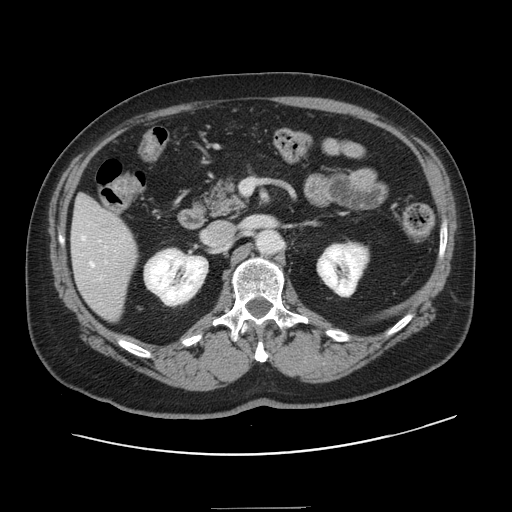
Contrast-enhanced abdominal CT, one axial slice; position 64 of 143 along the scan axis; 120 kVp; intravenous contrast given; soft-tissue window (W 400 / L 40 HU); 2.5 mm slice thickness; 512 × 512 image matrix. Male patient, age 62 years. Case-level facts recorded for this patient, not image findings: diagnosis: colorectal cancer liver metastases, imaged before liver resection; multiple liver metastases: yes; largest metastasis: 2.7 cm; disease in both lobes: no.
Annotated regions visible in this slice (expert manual segmentation):
- hepatic veins: bounding box [x1, y1, x2, y2] px = [82, 236, 94, 267]
- liver: [72, 197, 137, 321]
- planned liver remnant (the part of the liver to remain after resection): [77, 197, 95, 211]
- portal vein (with intrahepatic branches): [99, 241, 106, 248]